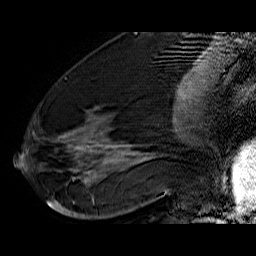
Breast MRI (dynamic contrast-enhanced), one sagittal slice. Position 26 of 60 along the scan axis. Dynamic contrast-enhanced series, time point 2 of 6 at this slice position (early post-contrast). 1.5 T. TE 6.4 ms, TR 32.9 ms. 4 mm slice thickness. 256 × 256 image matrix, field of view 200 × 200 mm. Female patient. Case-level facts recorded for this patient, not image findings: setting: breast cancer imaged before/during neoadjuvant chemotherapy; receptor status: HR-positive, HER2-negative.
Annotated regions visible in this slice (semi-automatically segmented with operator editing):
- analysis volume of interest (the breast-tissue region the enhancement analysis was run in; not a lesion): bounding box <40,74,176,210> (left, top, right, bottom; pixels)
- tumour enhancement mask (voxels above the 100 % enhancement threshold inside the analysis volume of interest): <47,133,143,206>